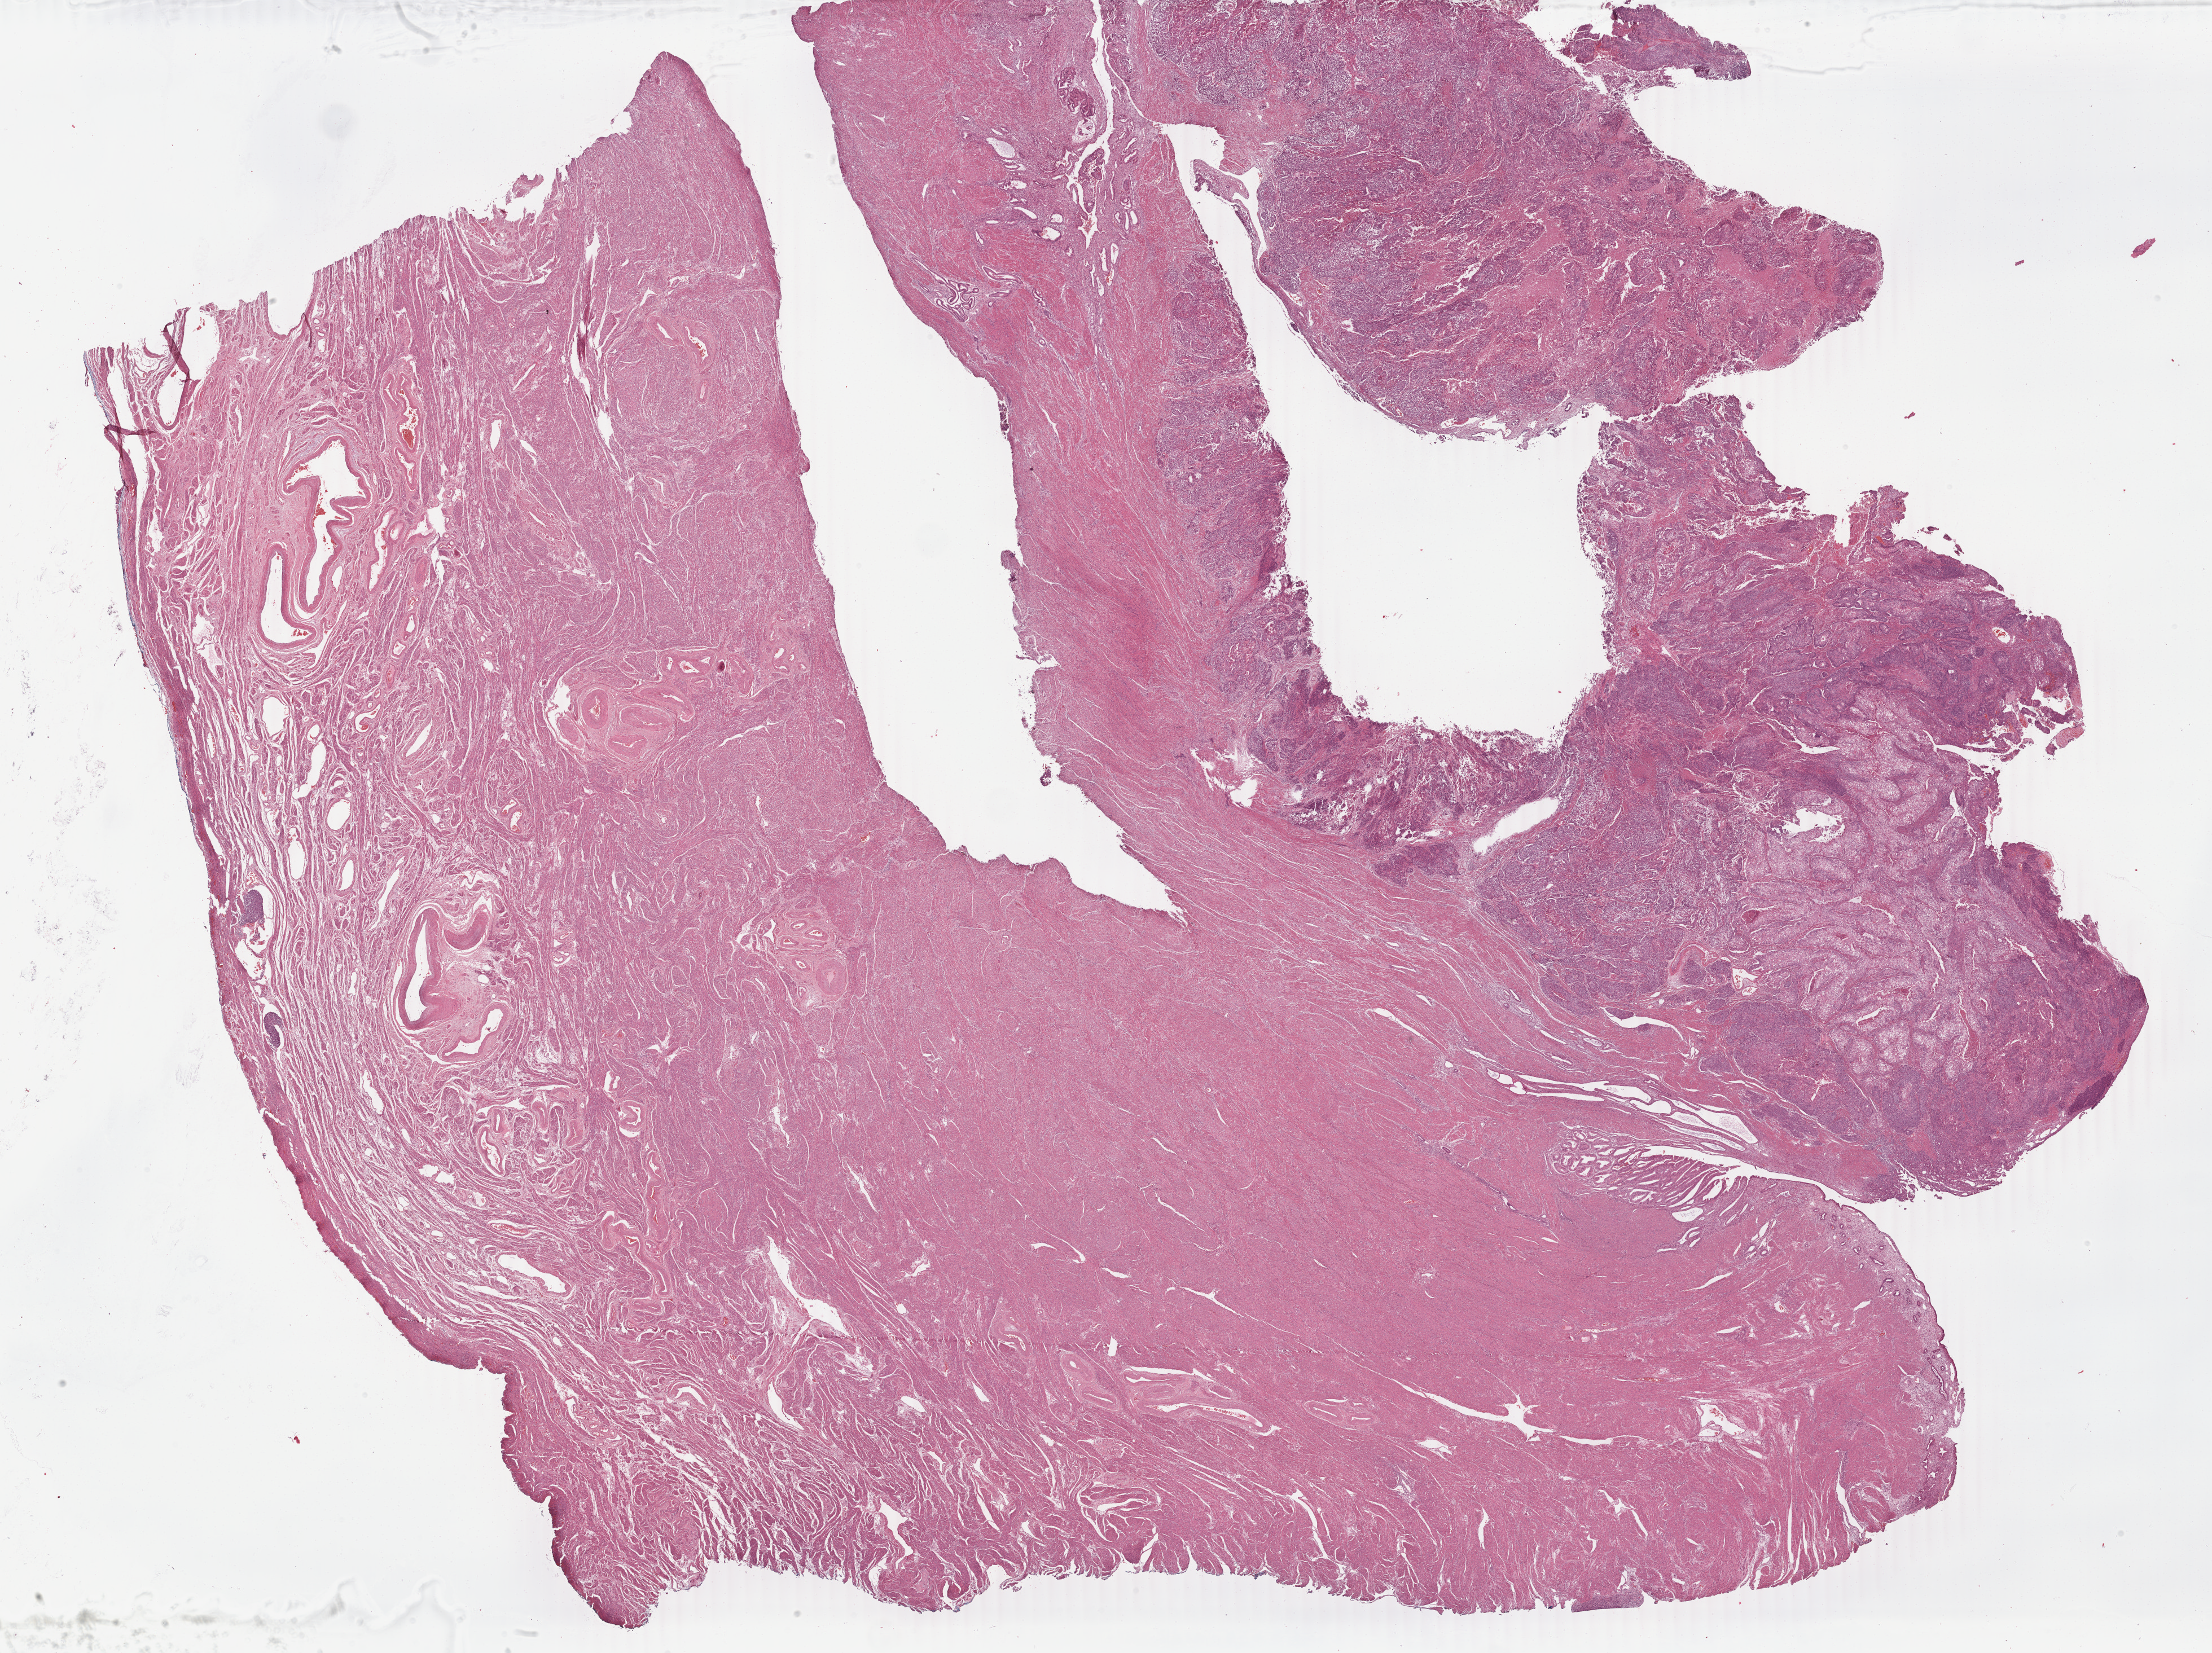
Hematoxylin and eosin (H&E) stained whole-slide image, low-resolution overview of the scanned area, about 31.2 x 23.3 mm, formalin-fixed paraffin-embedded (FFPE) diagnostic section, uterus, primary tumour sample. Patient: female, age at initial diagnosis 59 years. Histologic grade: G3 (poorly differentiated).
Pathologic diagnosis: Endometrioid adenocarcinoma, NOS (endometrium). FIGO stage: IC.